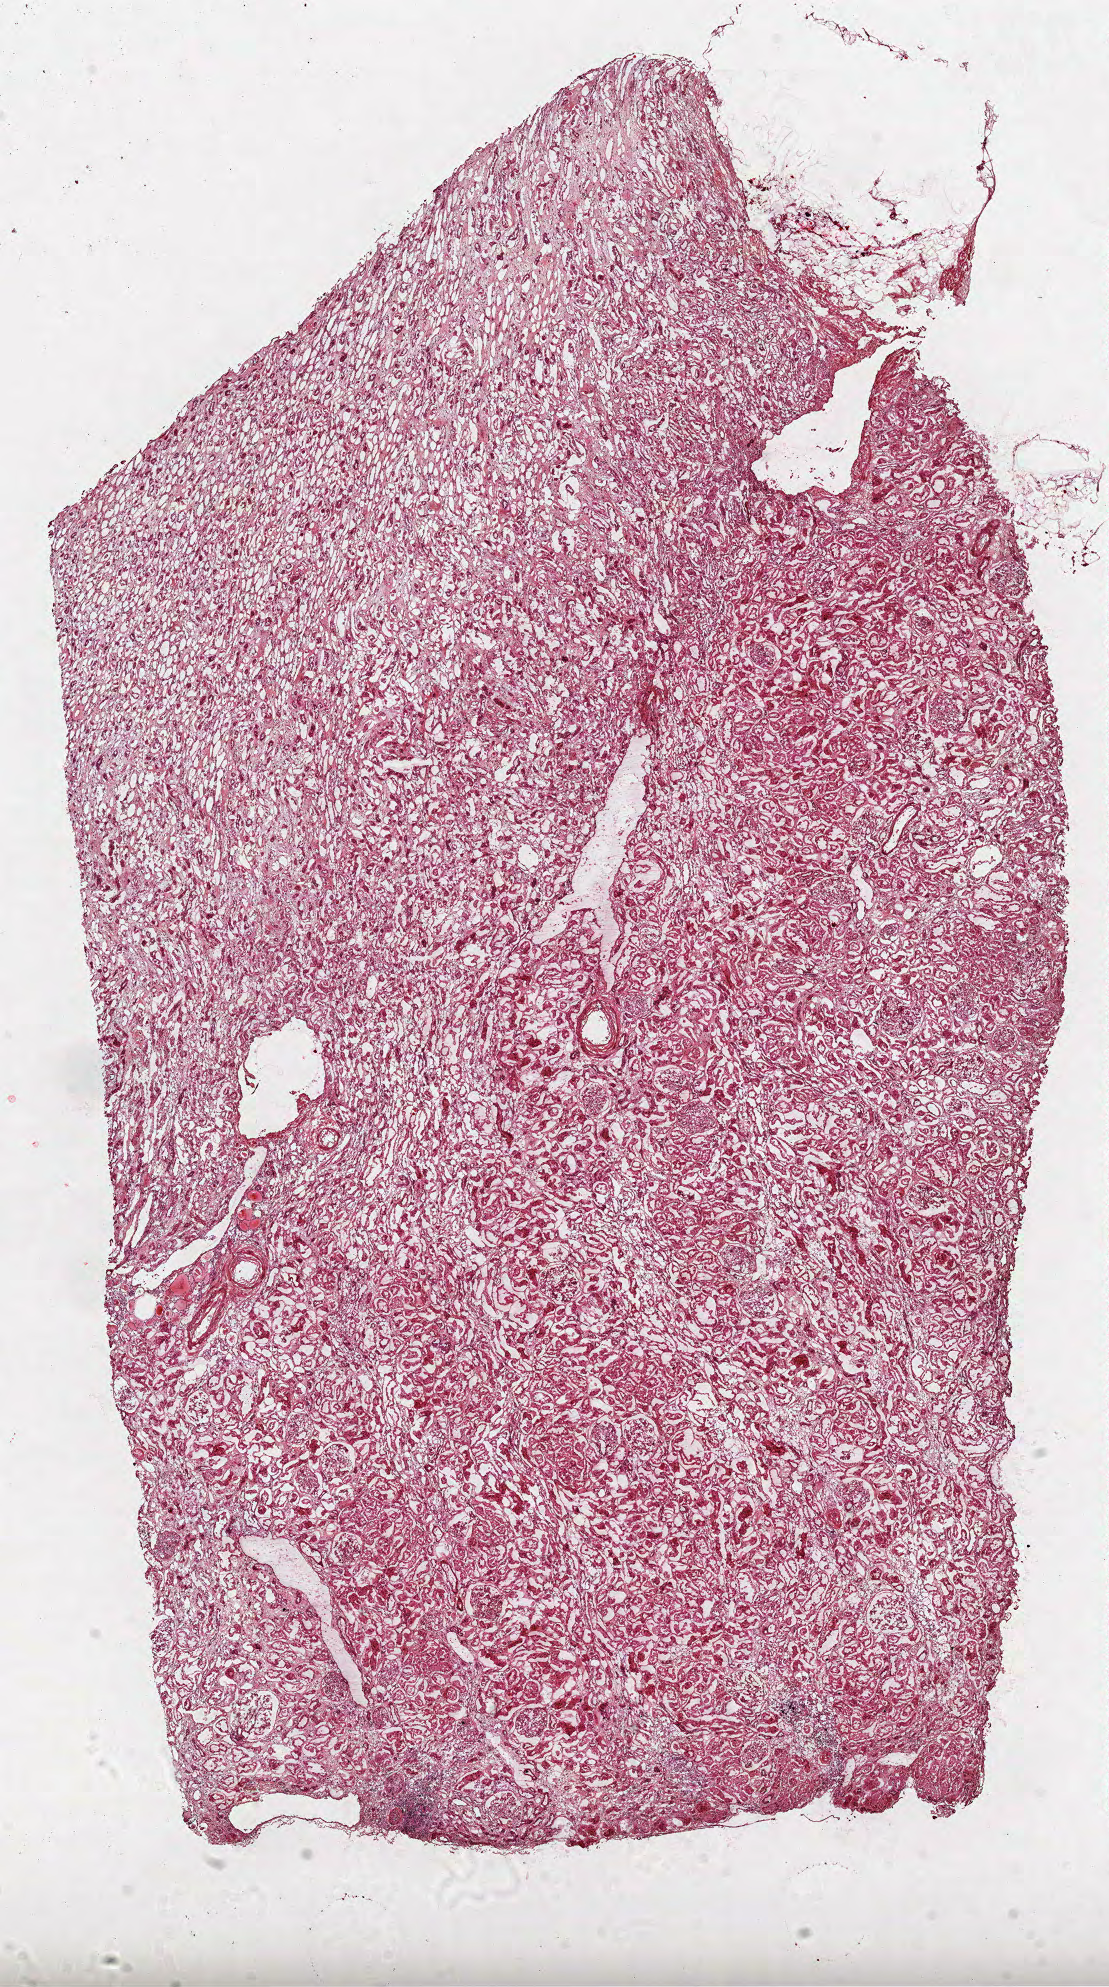
H&E-stained whole-slide image — shown as a low-resolution overview of the whole scanned area (about 8.9 x 16.0 mm, acquisition: 40x scan), frozen section from the top of the tissue portion, solid tissue normal (non-tumour tissue) sample from the kidney. Female patient; age at initial diagnosis 75 years.
This section: solid tissue normal (non-tumour) sample from the same patient. Patient diagnosis: Papillary adenocarcinoma, NOS.